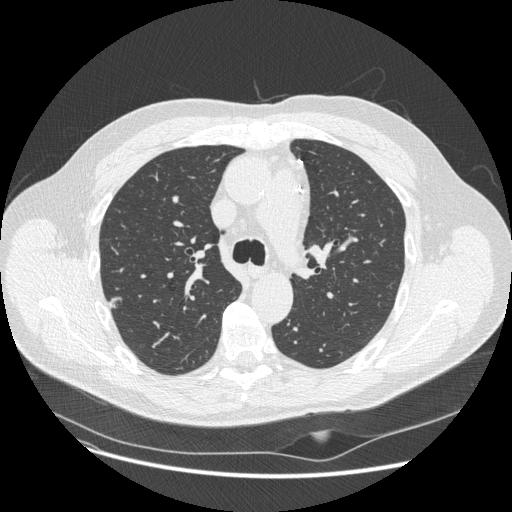
Low-dose screening chest CT, axial slice; second screening round (one year after baseline); lung window (W 1500 / L -600 HU); 1.25 mm slice thickness; 512 × 512 image matrix, field of view 400 × 400 mm. Male participant, aged 62 years at enrolment. Current smoker at enrolment.
Expert reader's lesion annotation, bounding box <99,291,129,317> (left, top, right, bottom; pixels). The exam's reader record, not a measurement of the box and not confirmed to be the same lesion: non-calcified nodule or mass ≥4 mm, right upper lobe, 11 × 7 mm, smooth margins, pre-existing on the prior screen: yes. Later outcome: lung cancer diagnosed 482 days after this screen — adenocarcinoma, NOS, right upper lobe, moderately differentiated (G2), stage IA (AJCC 6th edition), 12 mm at pathology.